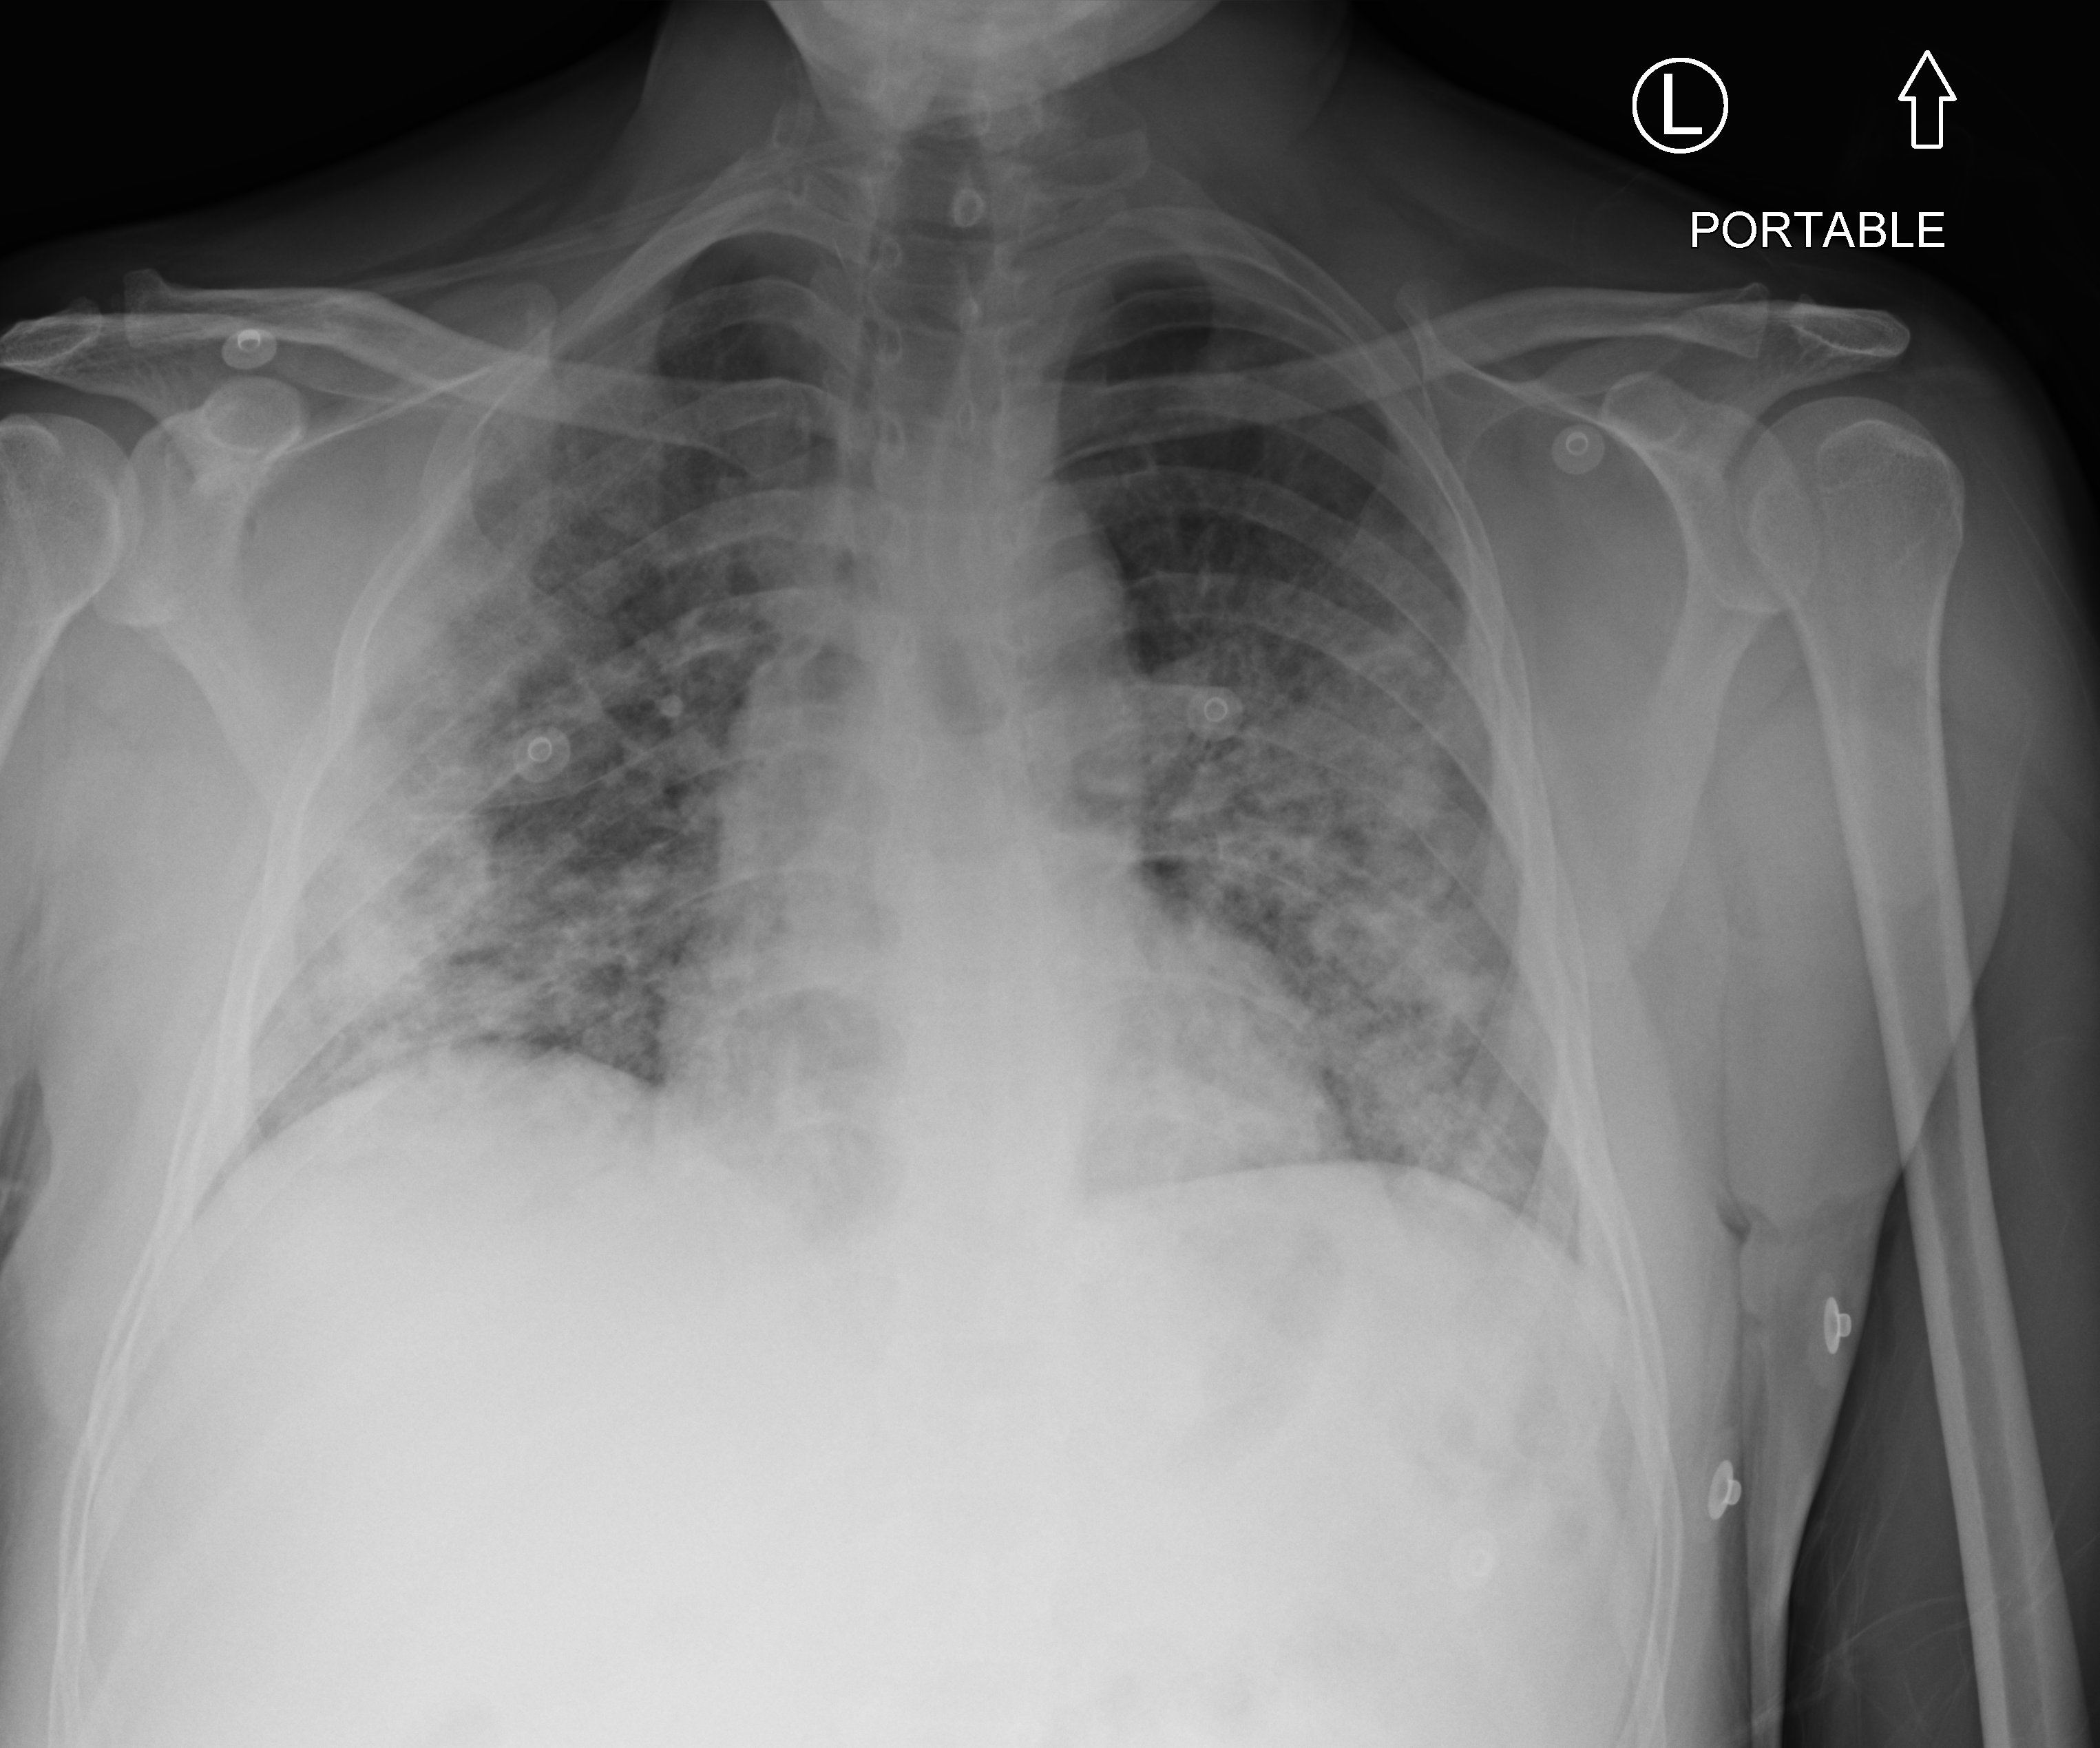
Bedside chest radiograph (computed radiography), anteroposterior (AP) projection. Adult patient hospitalised with COVID-19, age 18–59 years.
Admission-level facts for this patient (not findings on this image; timing relative to this image not recorded):
- COPD (admission record): no